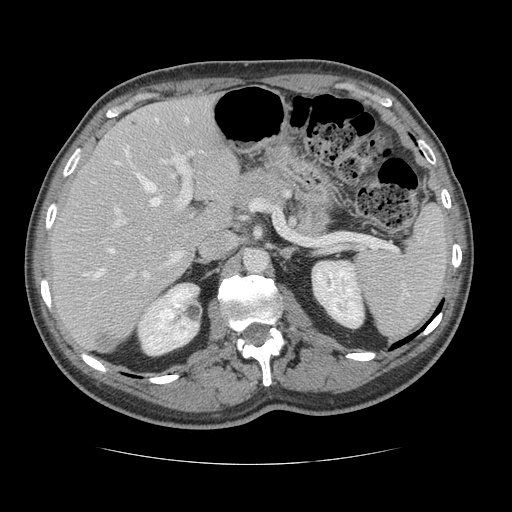
Contrast-enhanced abdominal CT, one axial slice. Position 81 of 134 along the scan axis. Reconstruction kernel STANDARD. Intravenous contrast given. Soft-tissue window (W 400 / L 40 HU). 2.5 mm slice thickness. 512 × 512 image matrix, field of view 377 × 377 mm. Male patient, age 68 years. Case-level facts recorded for this patient, not image findings: diagnosis: colorectal cancer liver metastases, imaged before liver resection.
Structures marked on this image (manually delineated by an expert):
- hepatic veins: bounding box <83,119,202,277> (left, top, right, bottom; pixels)
- liver: <51,96,241,352>
- planned liver remnant (the part of the liver to remain after resection): <52,96,241,338>
- portal vein (with intrahepatic branches): <114,117,195,277>
- liver metastasis: <96,332,118,351>